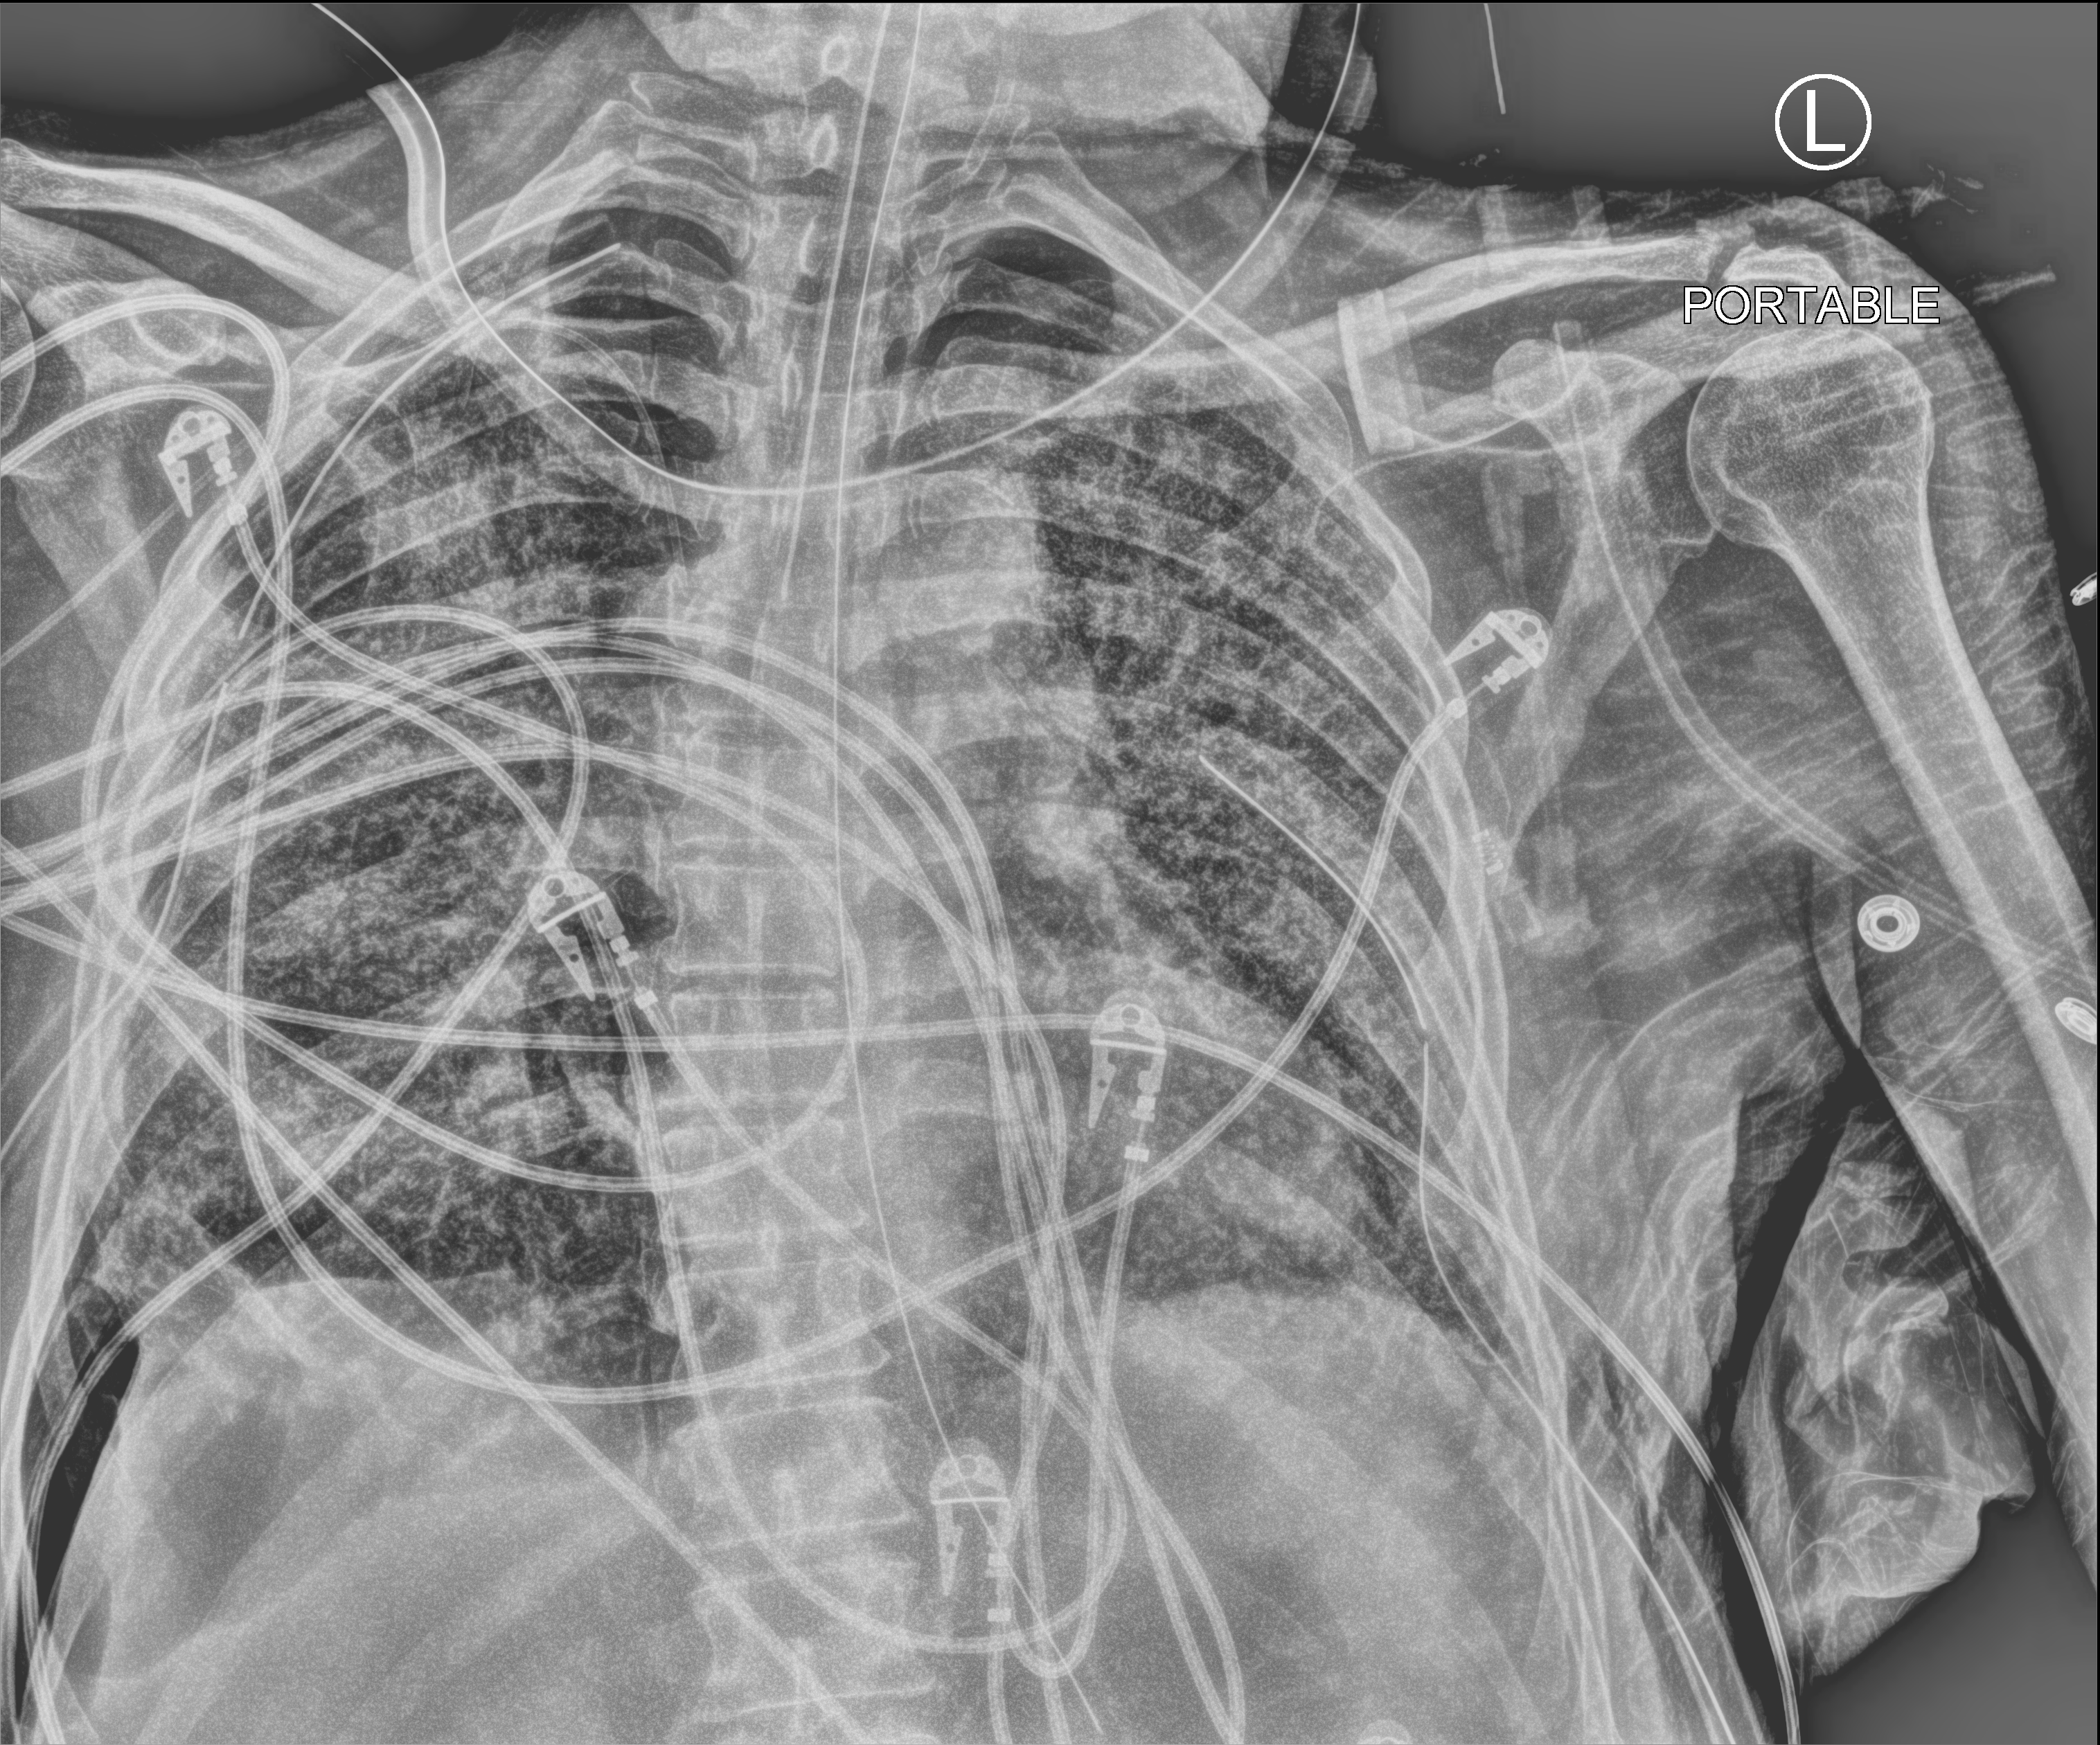
Bedside chest radiograph (computed radiography); anteroposterior (AP) projection. Male patient hospitalised with COVID-19, age 60–74 years.
Hospital-stay facts (about this admission, not read from this image; timing relative to this image not recorded):
- mechanically ventilated during this hospital stay: yes